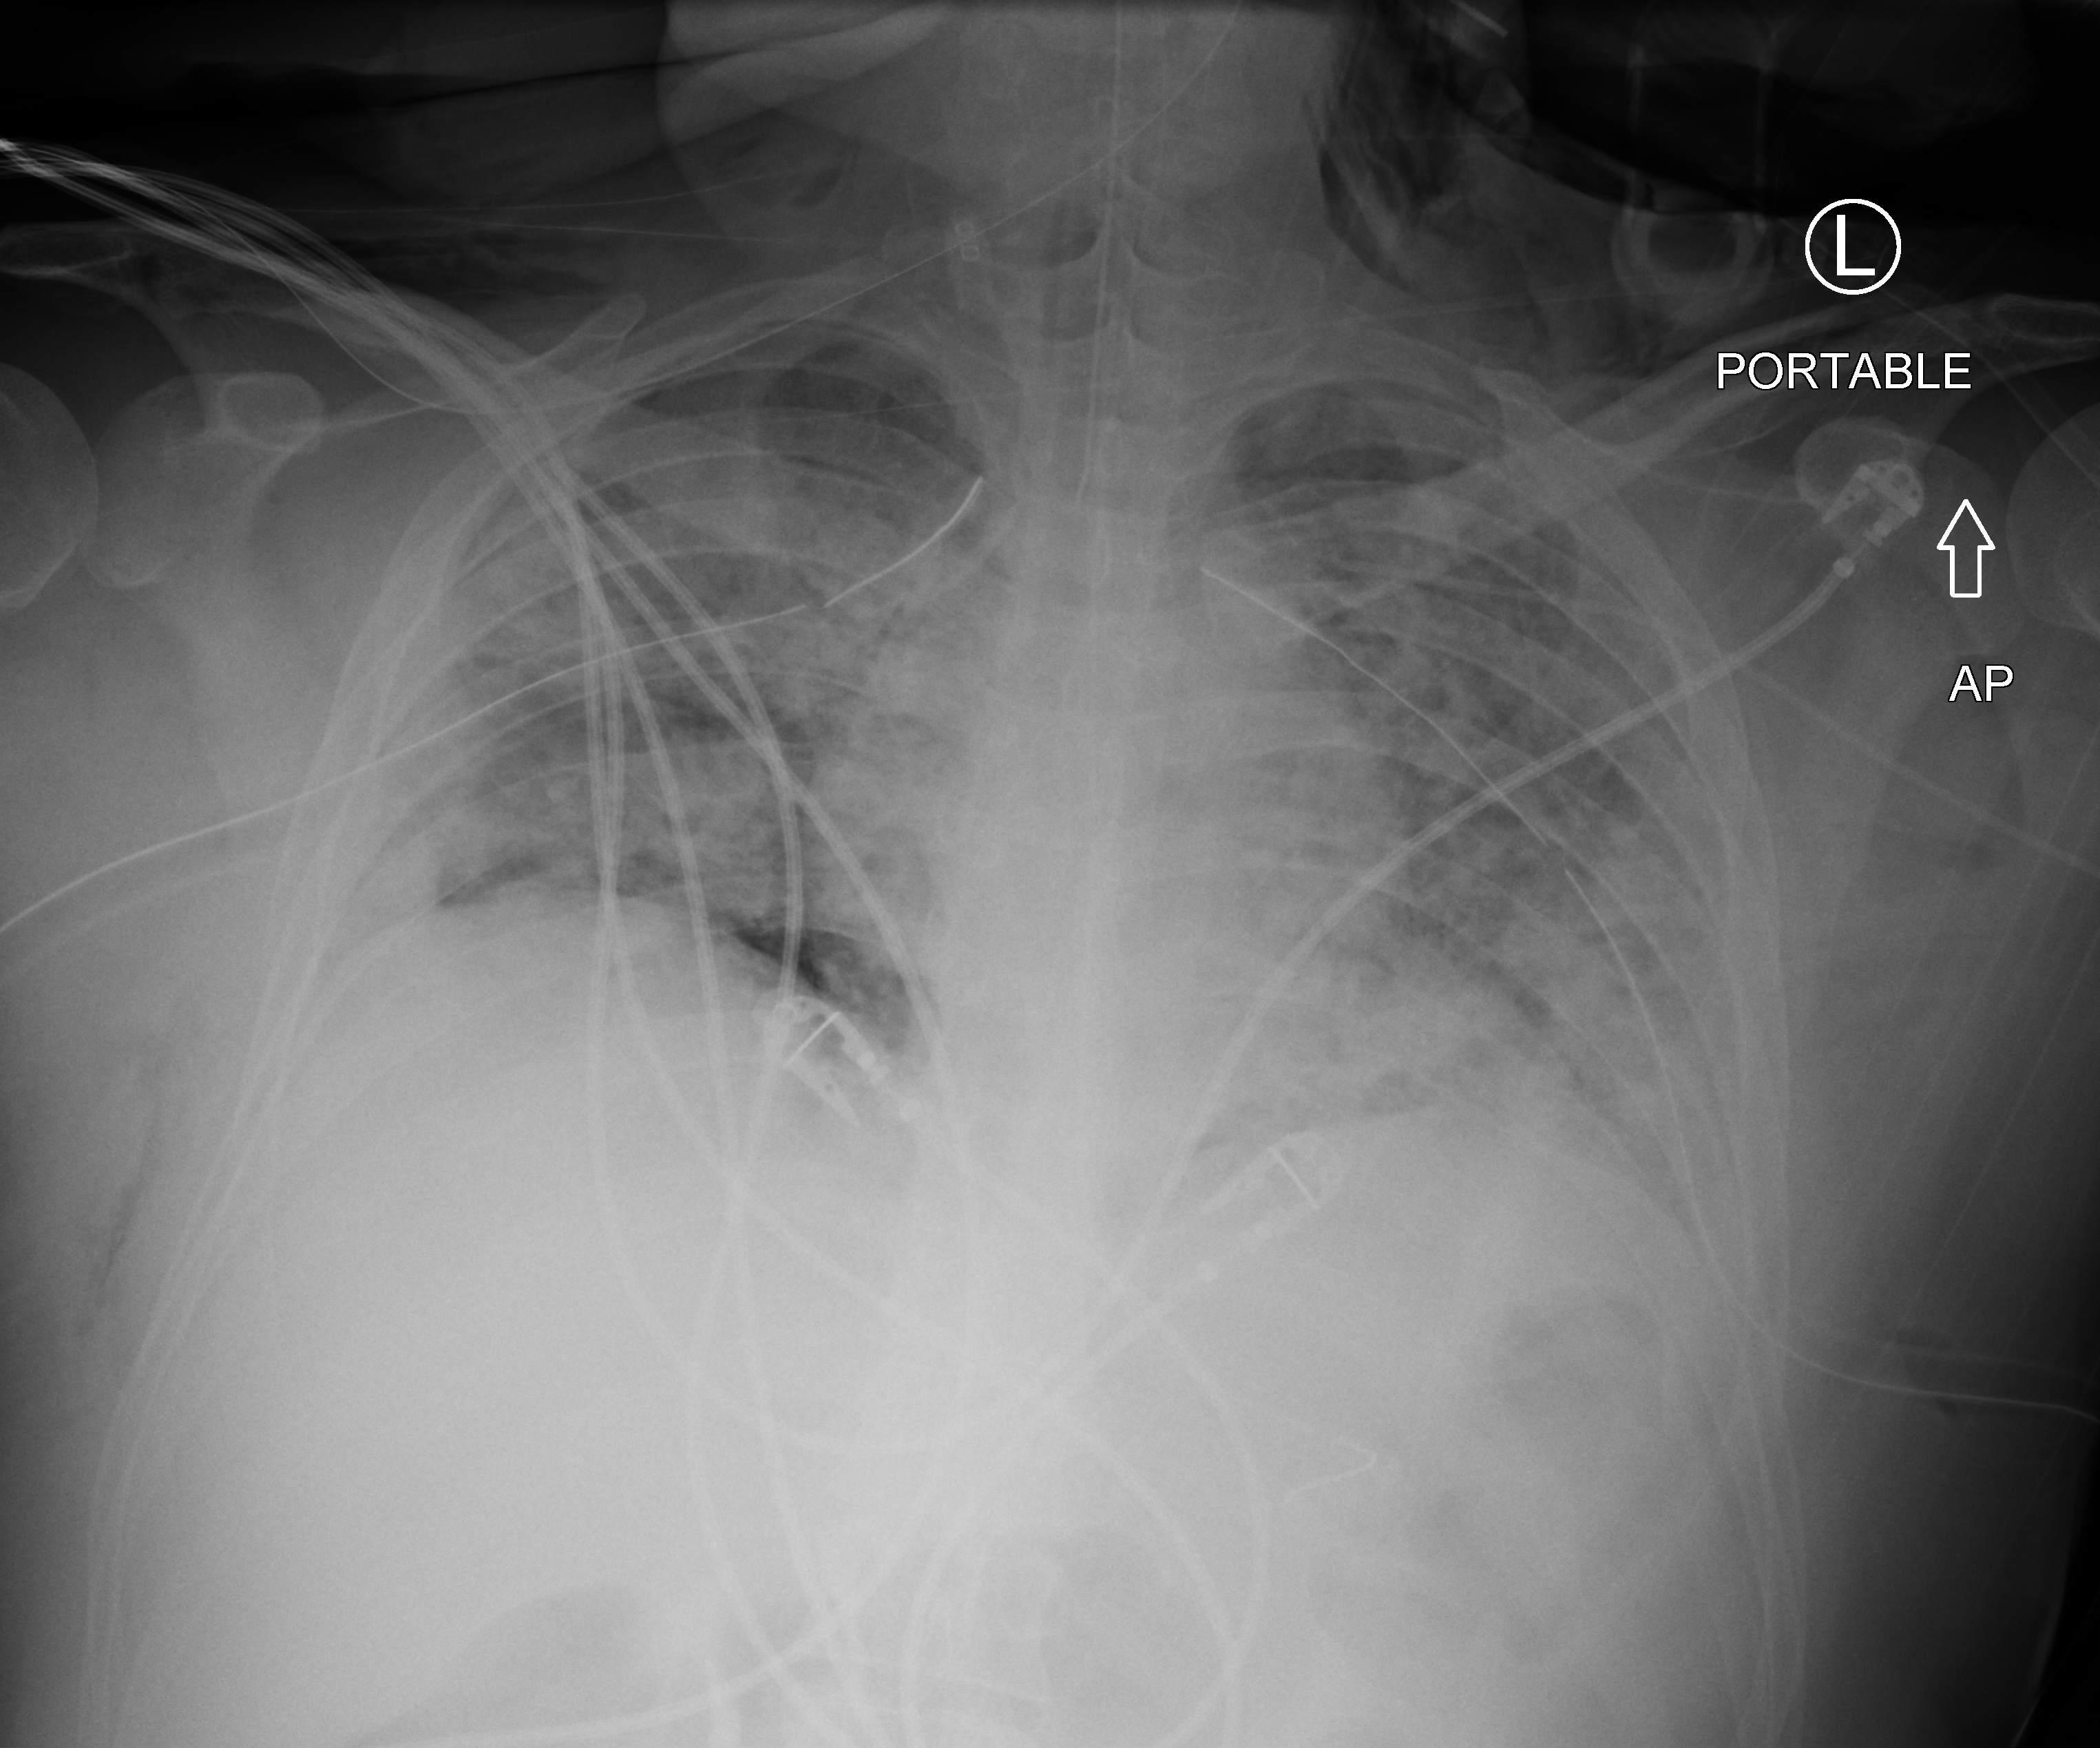
Bedside chest radiograph (computed radiography); anteroposterior (AP) projection. Patient hospitalised with COVID-19; male, aged 18–59 years.
Admission-level facts for this patient (not findings on this image; timing relative to this image not recorded): mechanically ventilated during this hospital stay: yes.